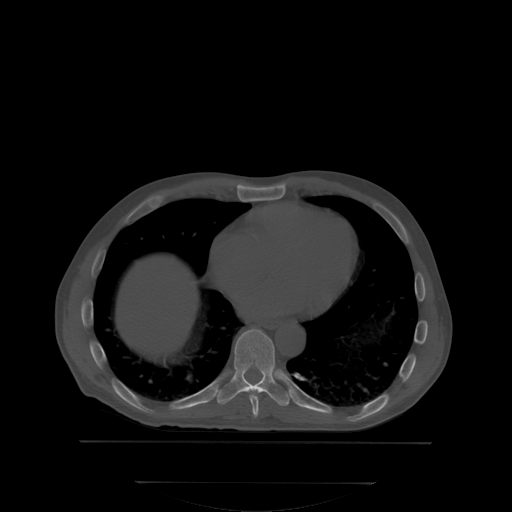
CT including the spine, one axial slice. Position 207 of 350 along the scan axis. Bone window (W 1800 / L 400 HU). 512 × 512 image matrix, field of view 500 × 500 mm. Patient: male, 58 years. Case-level facts recorded for this patient, not image findings: primary cancer: prostate; vertebrae with lytic lesions (as recorded): L1.
Annotated regions visible in this slice (semi-automatic segmentation, software-assisted and operator-edited):
- T8 vertebra: bounding box [x1, y1, x2, y2] px = [250, 391, 259, 416]
- T9 vertebra: [216, 329, 290, 406]